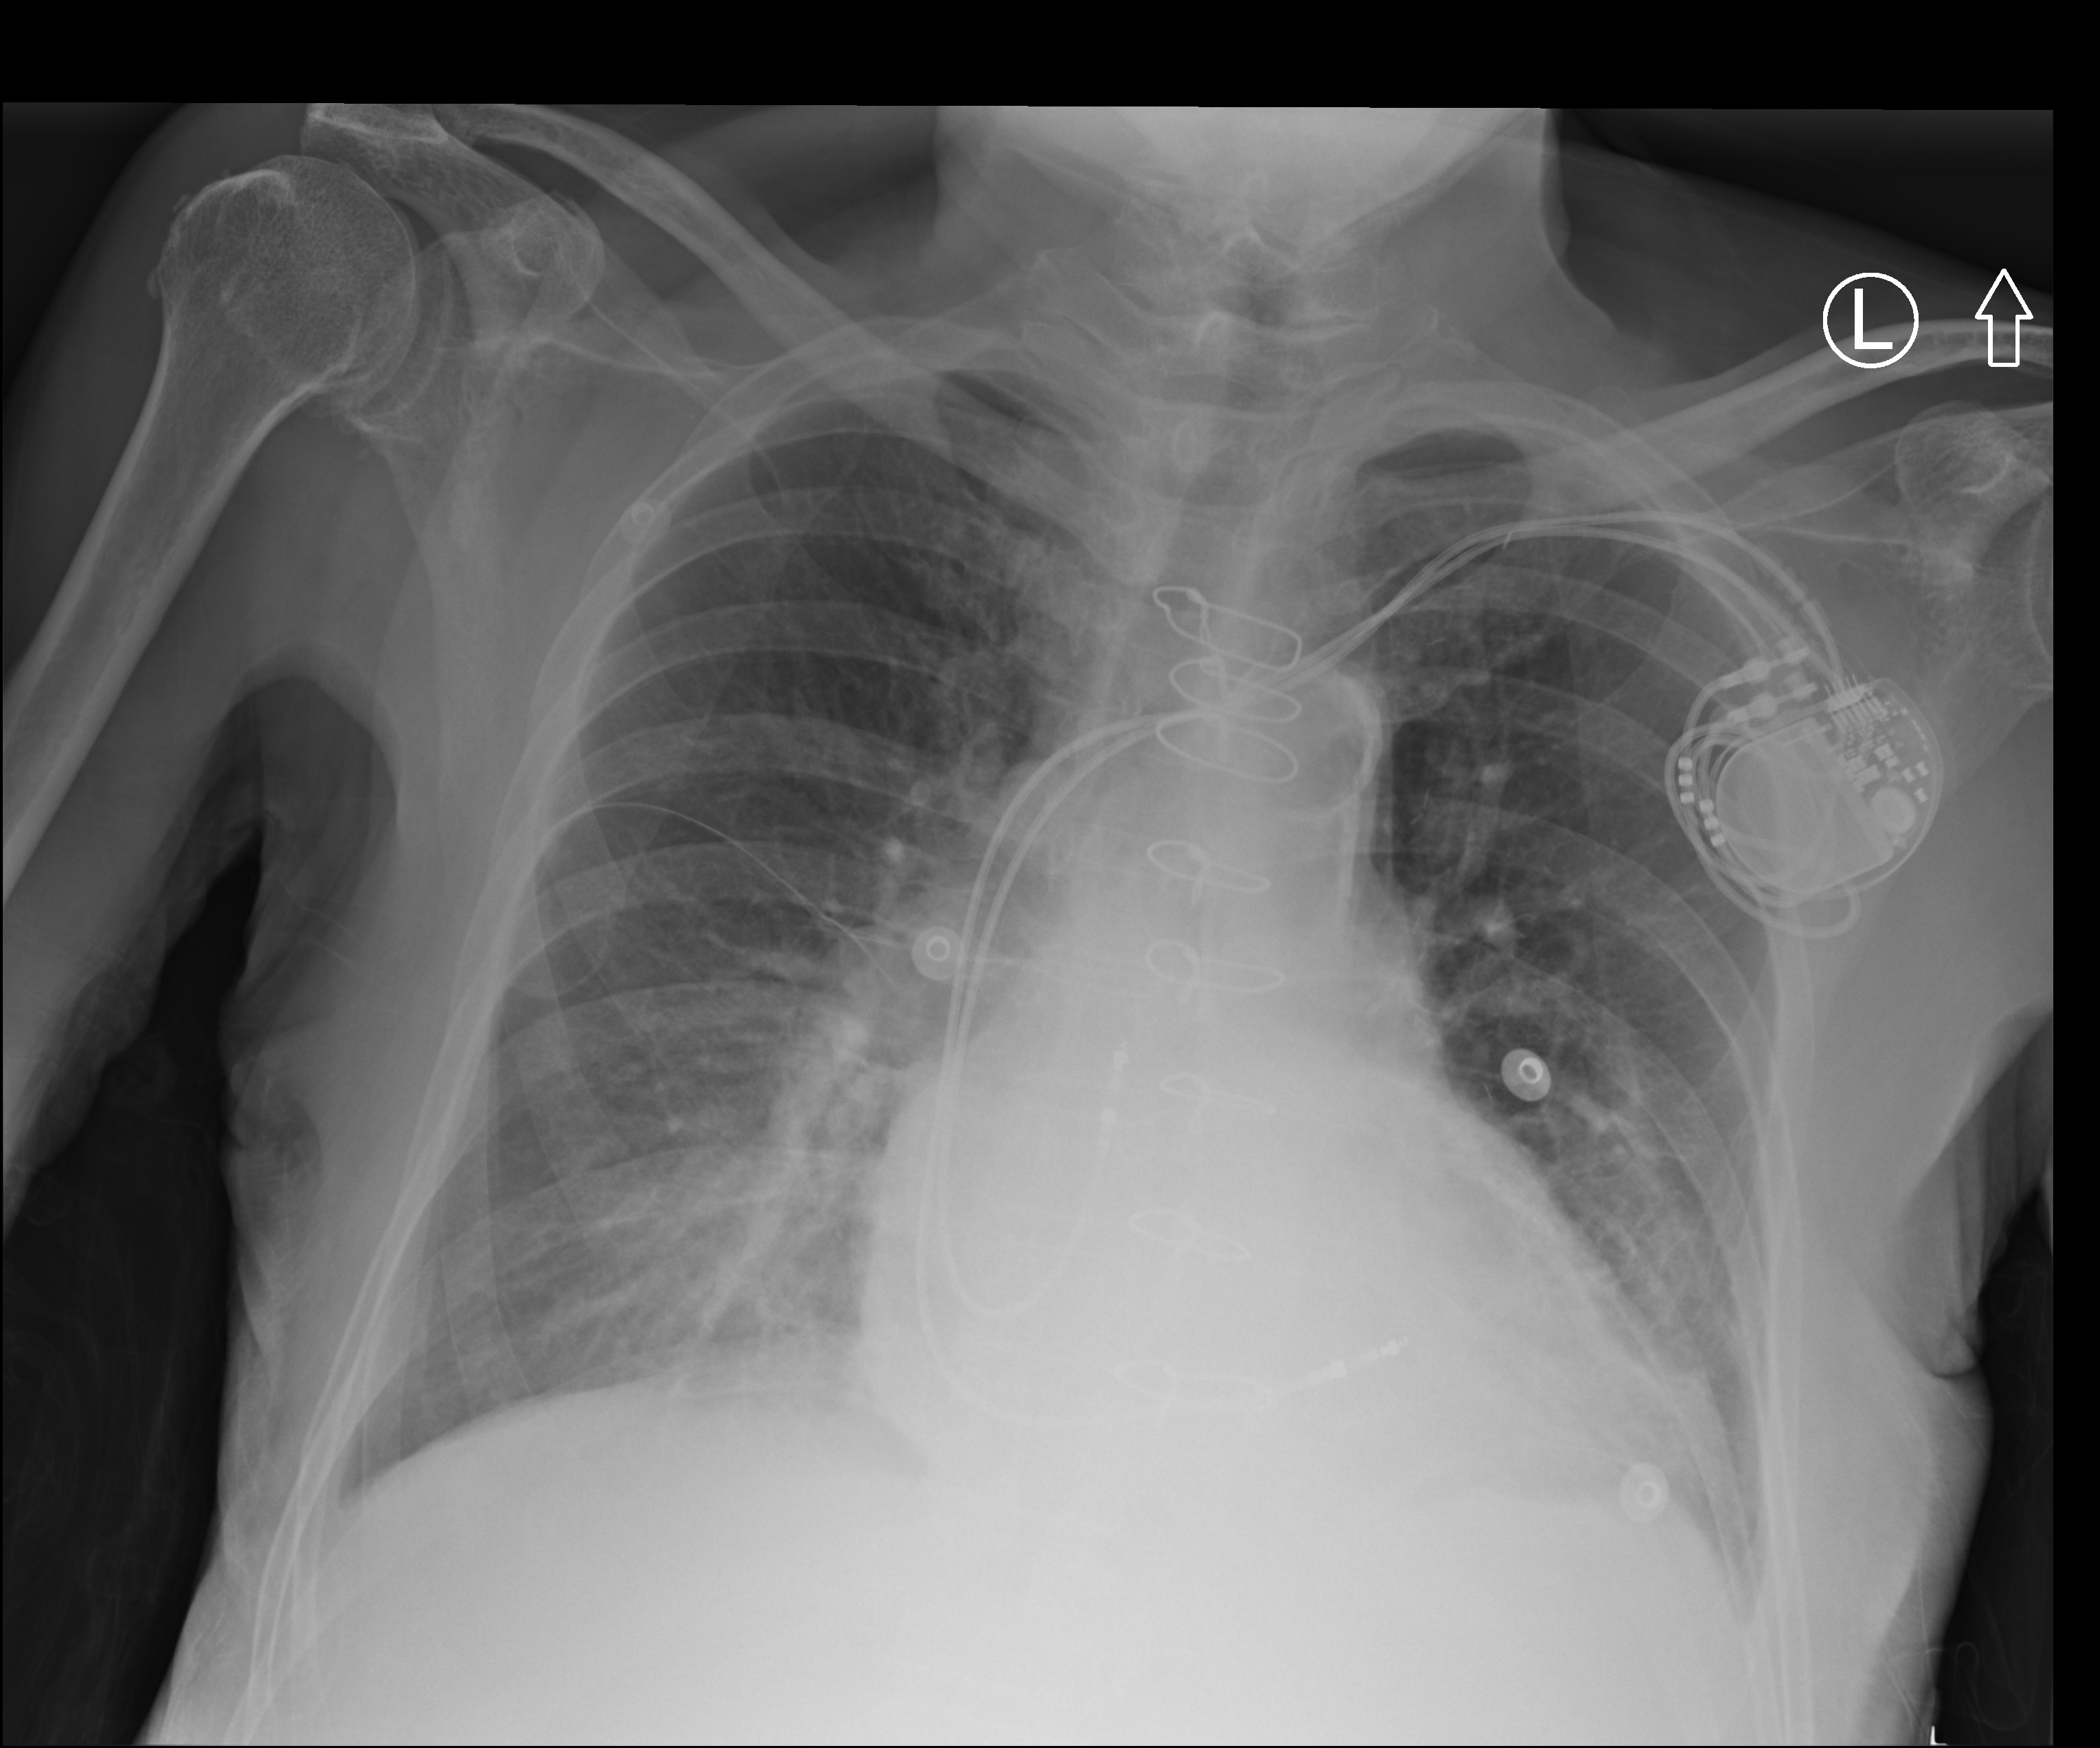
Chest X-ray, anteroposterior (AP) projection. Patient hospitalised with COVID-19; male, aged 60–74 years.
Hospital-stay facts (about this admission, not read from this image; timing relative to this image not recorded): admitted to intensive care during this hospital stay: no; diabetes (admission record): yes.